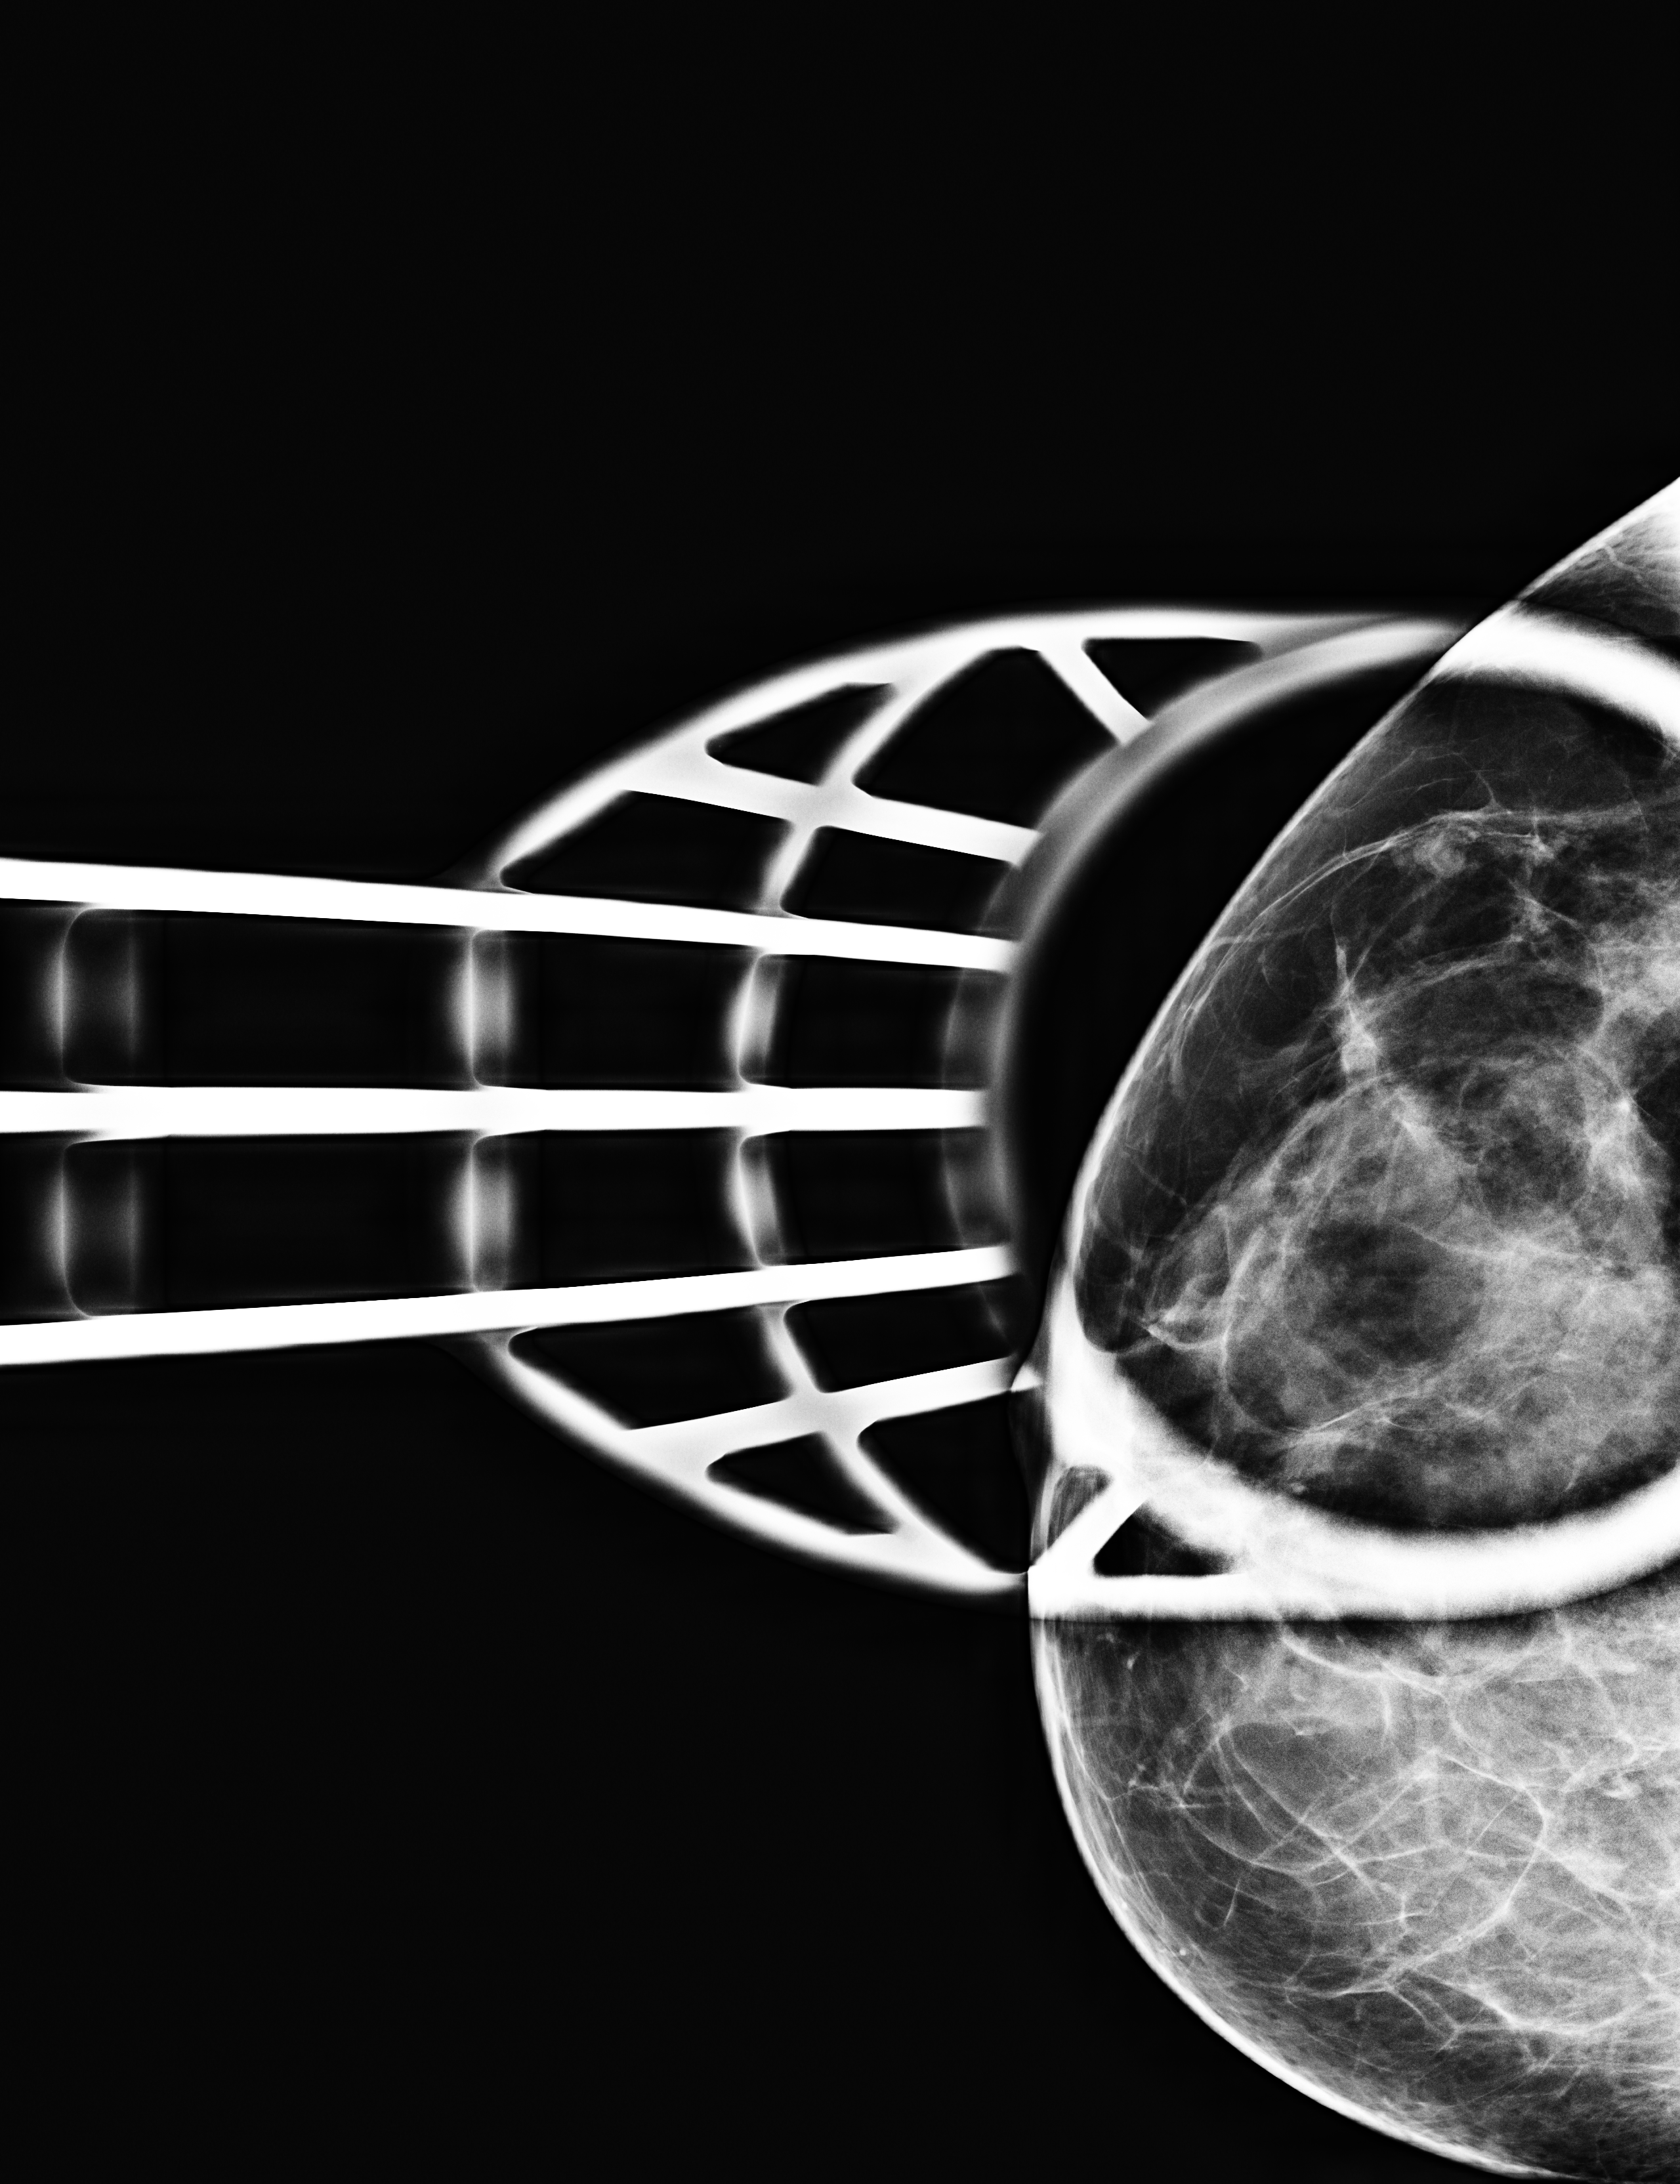
Additional (diagnostic) view. Patient aged 43 years (female).
Image type: full-field digital mammogram. Breast: right. Projection: CC view, spot compression.